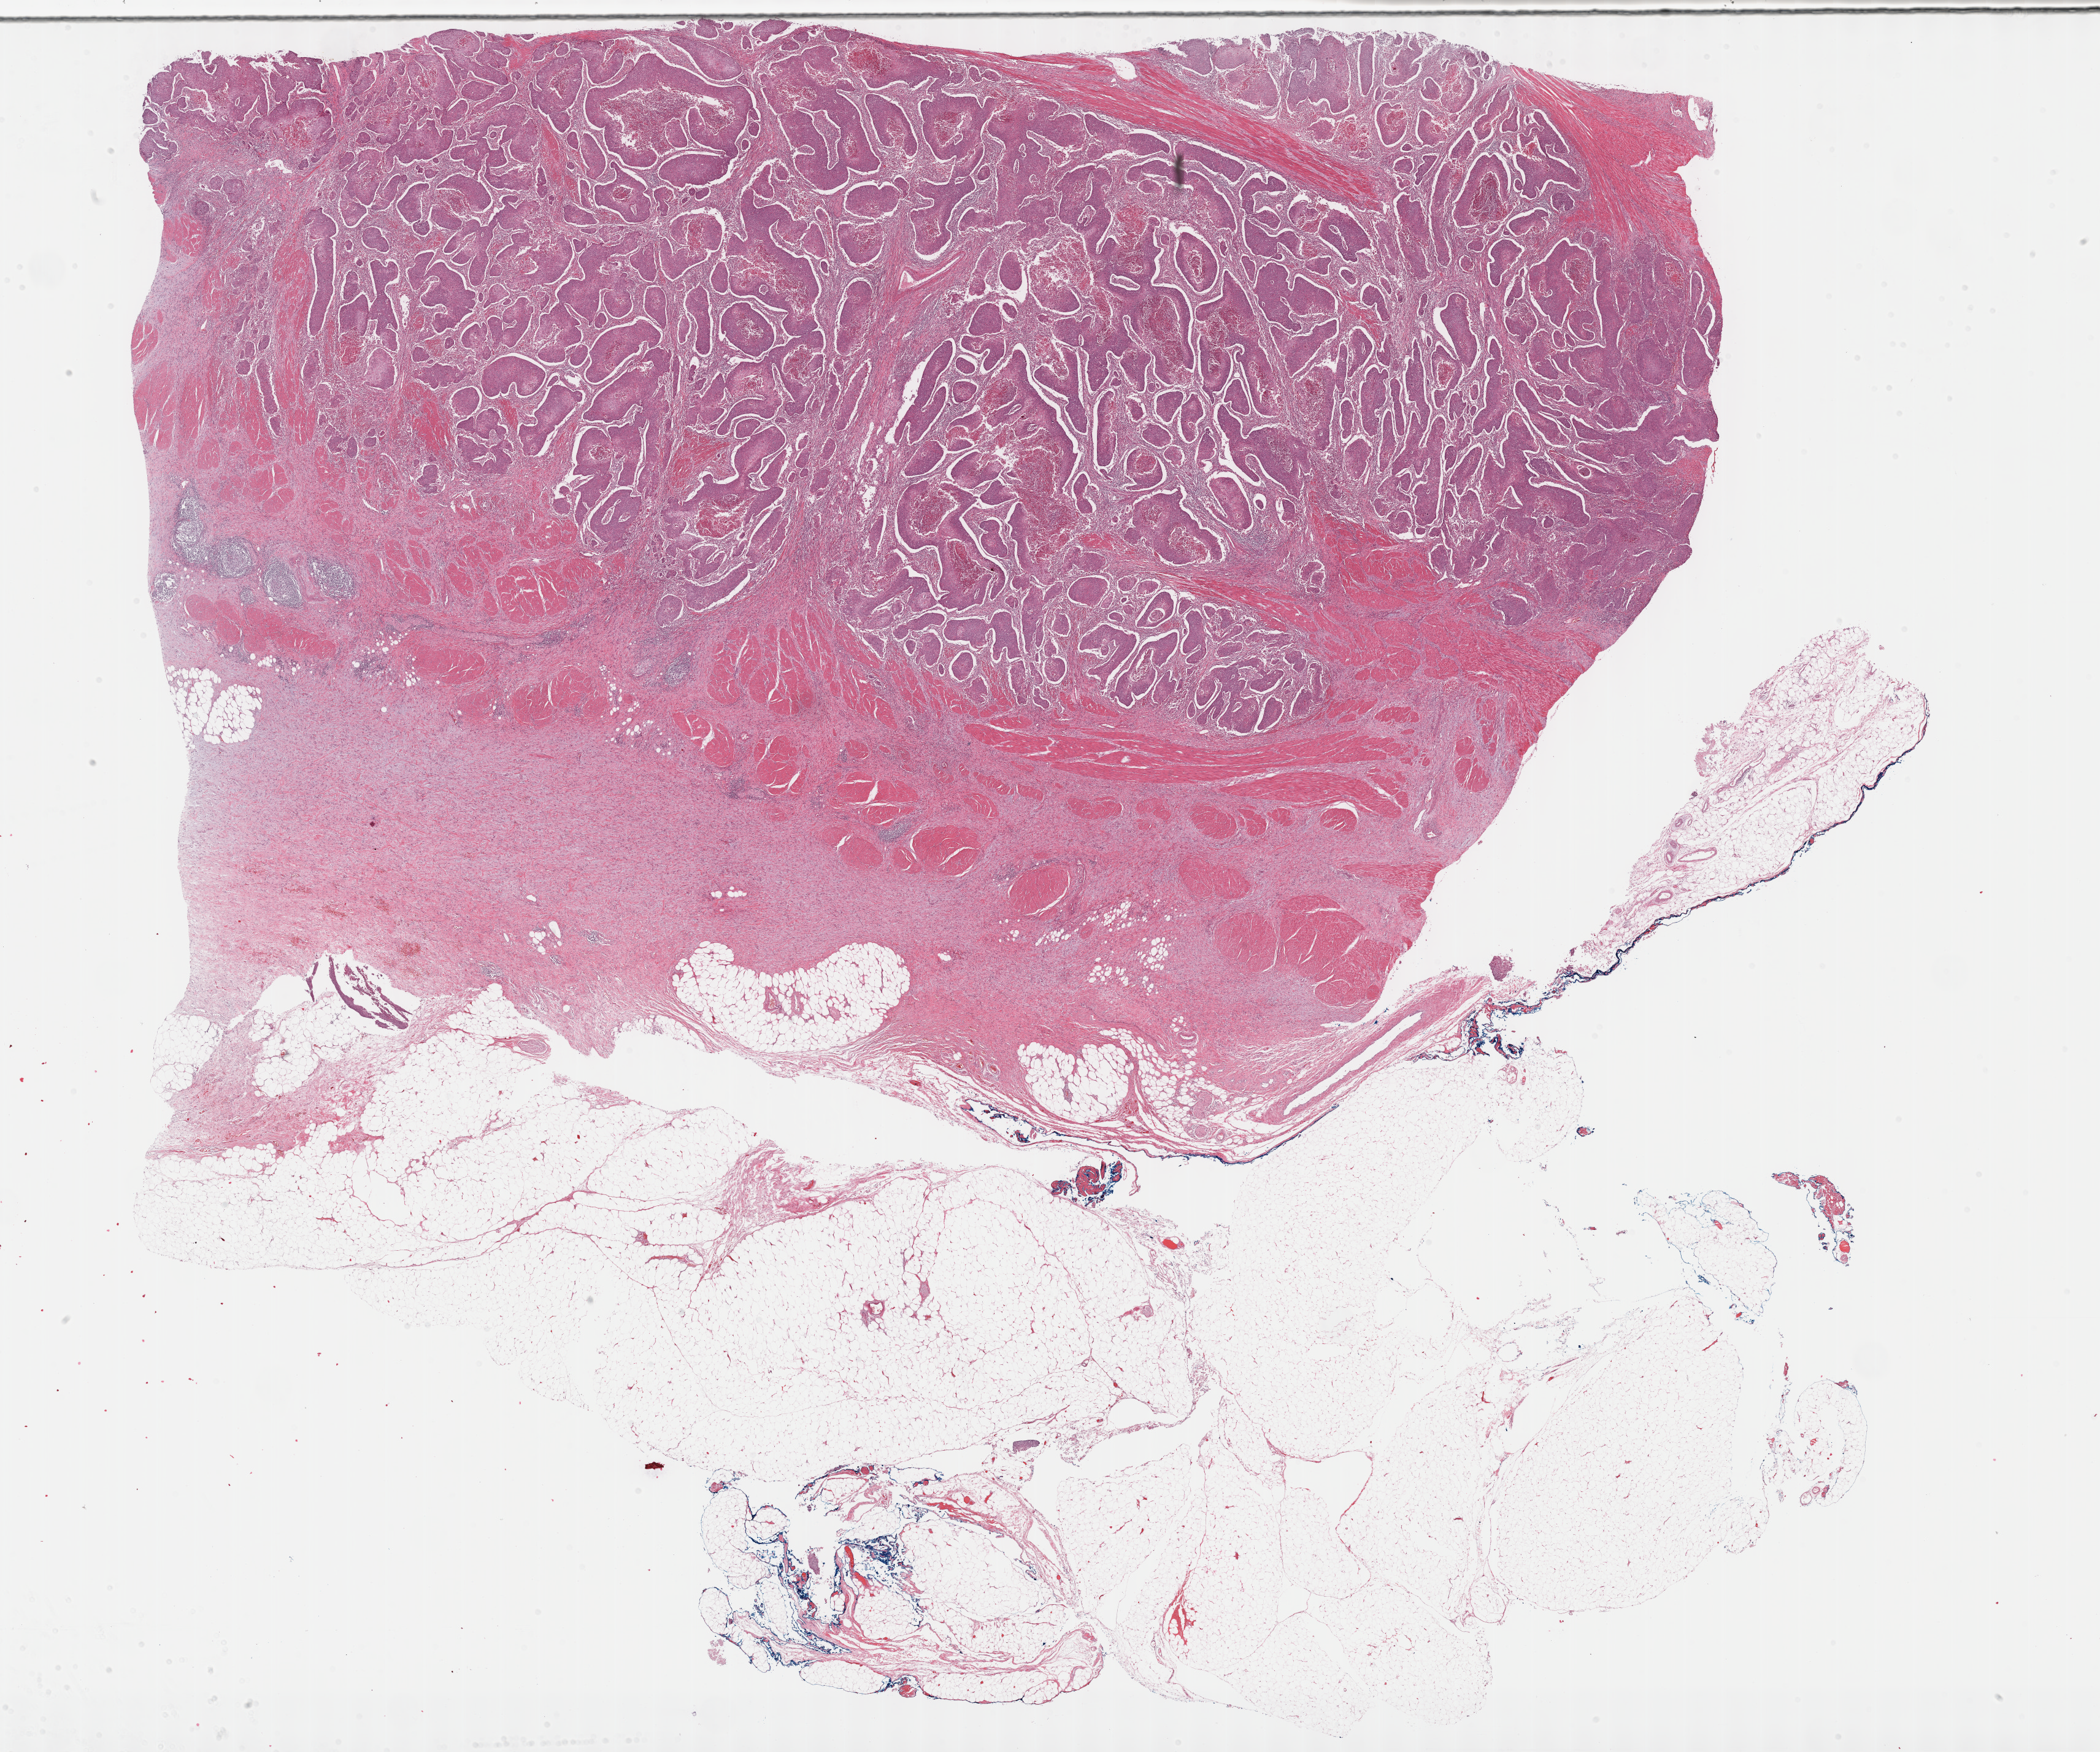
H&E whole-slide image, shown as a low-resolution overview of the whole scanned area (about 27.7 x 23.1 mm, from a 40x scan); FFPE section; bladder, primary tumour sample. Male, age 47 years at initial diagnosis. Histologic grade: high grade.
- TNM: T3b N0 MX
- AJCC pathologic stage: III (6th edition)
- diagnosis: Transitional cell carcinoma
- lymph nodes positive (case pathology): 0 of 77 examined